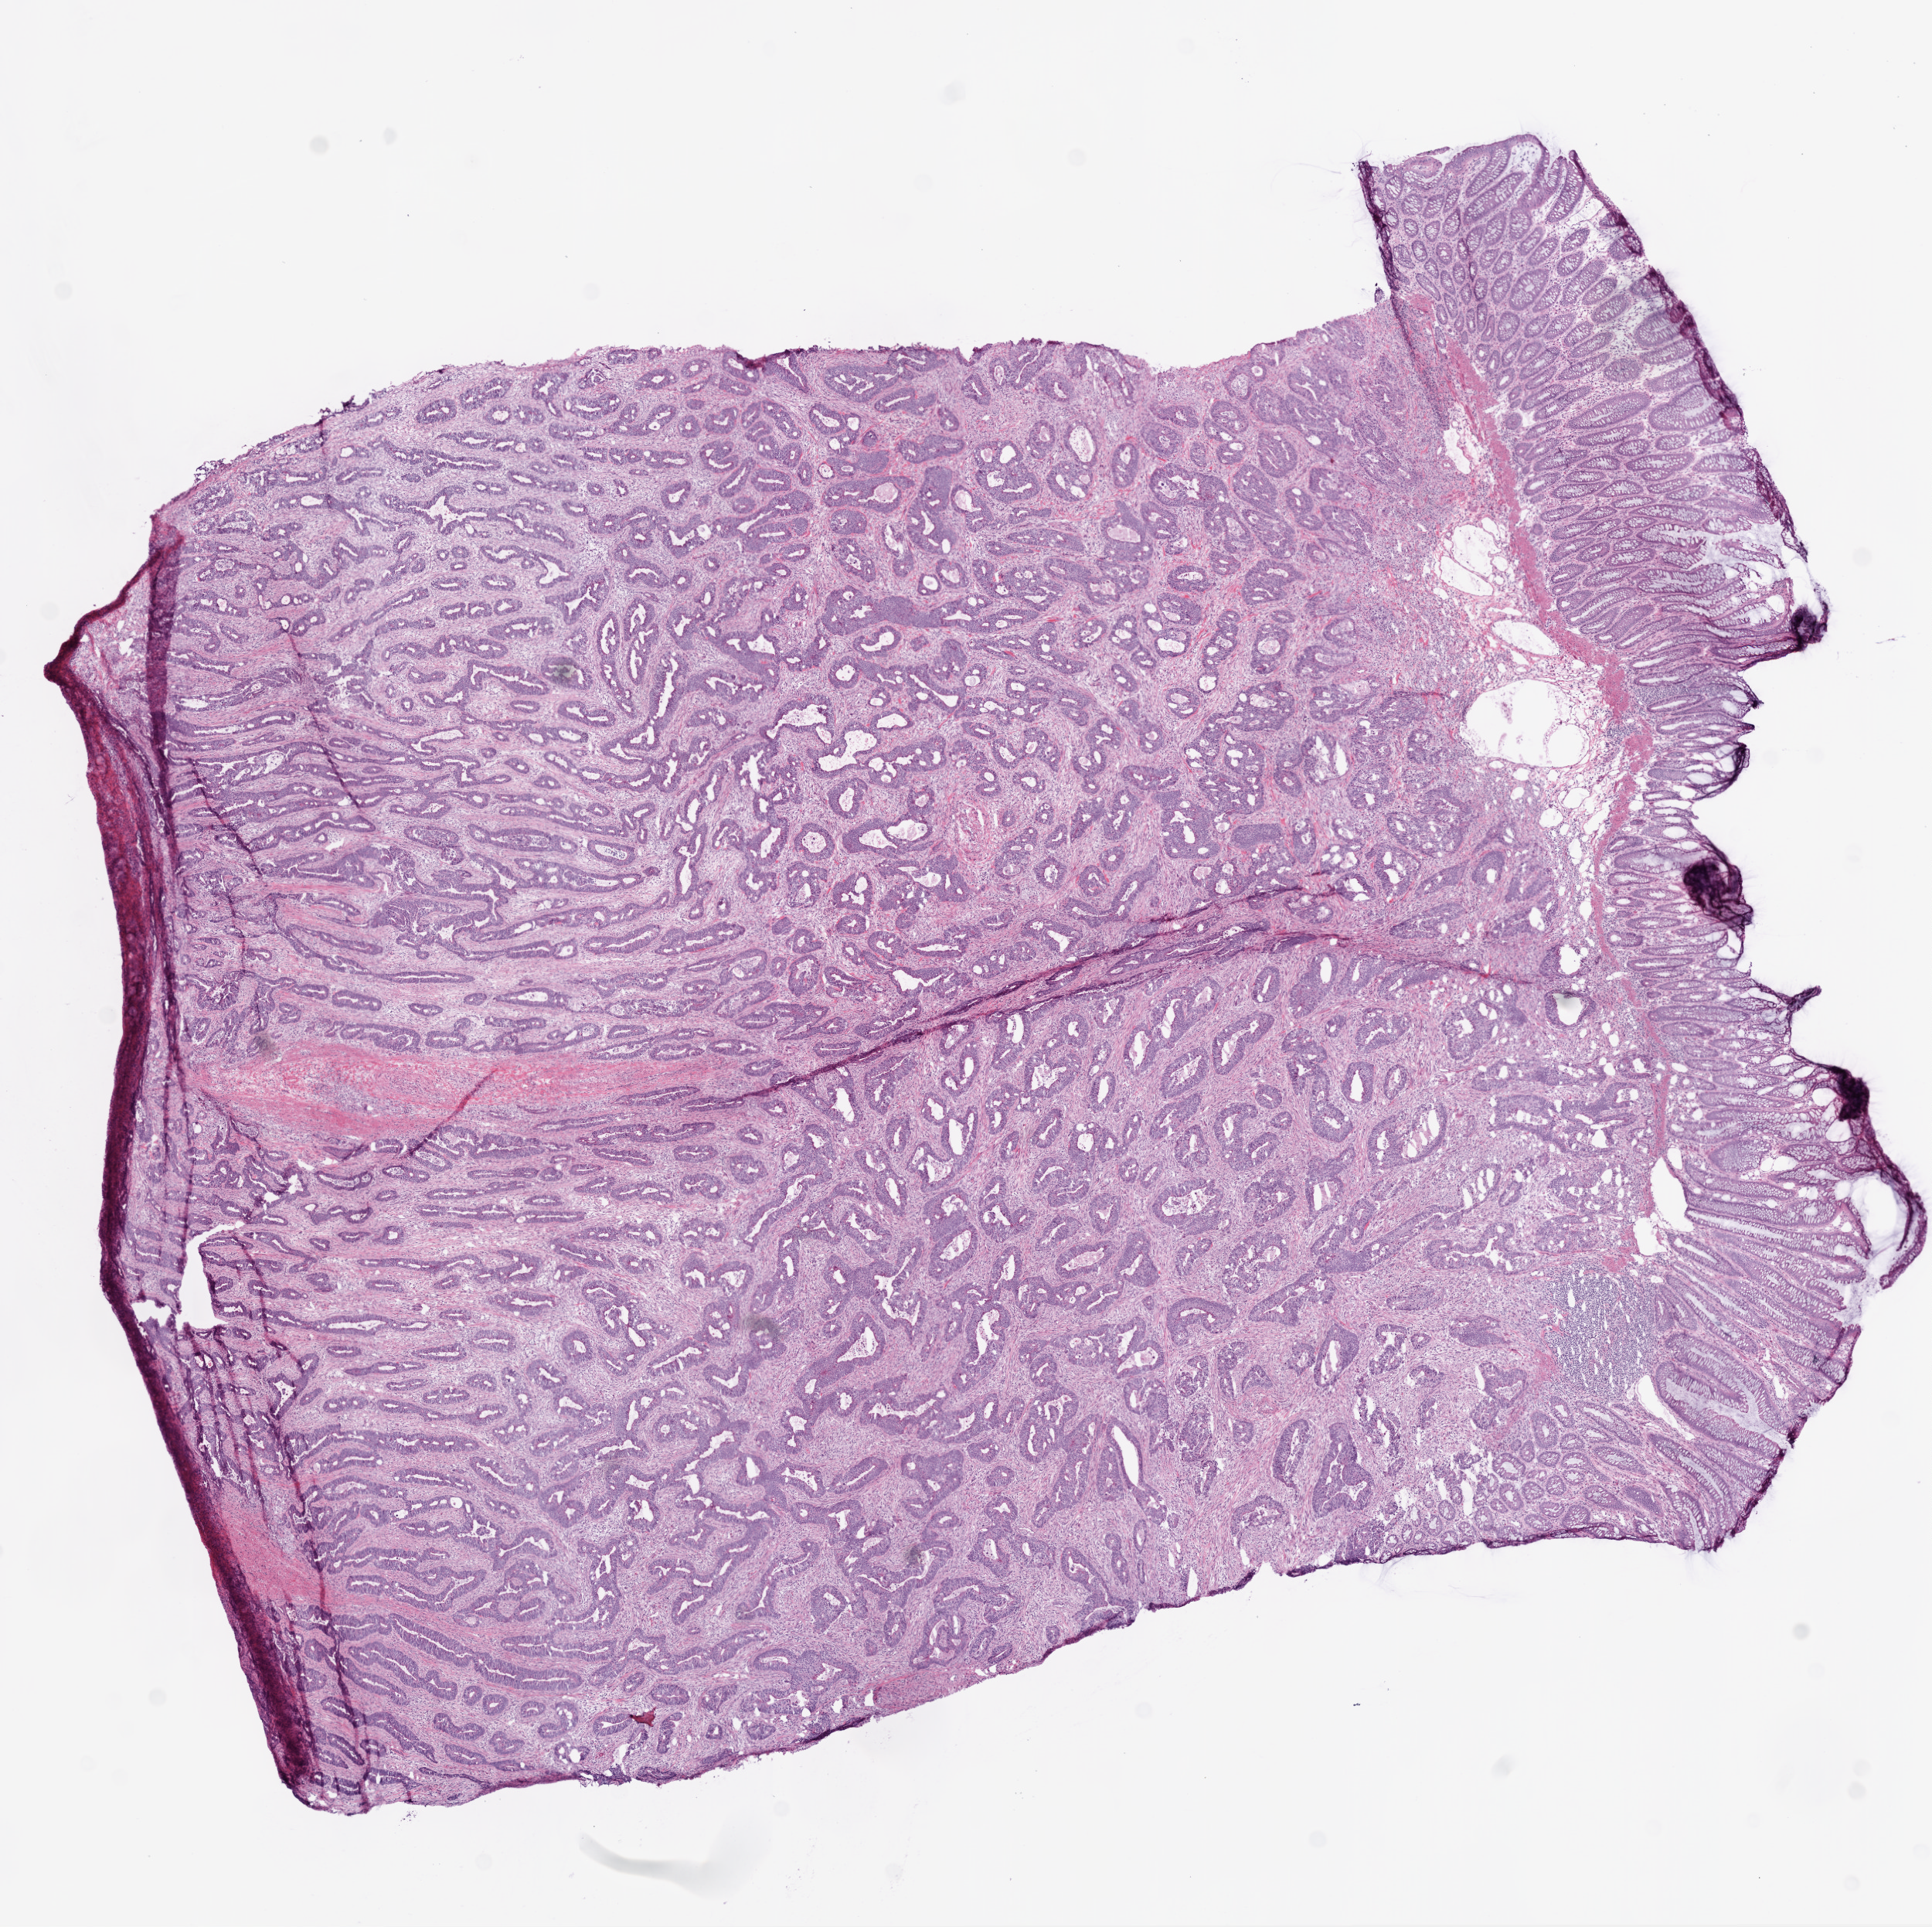
Whole-slide histology image, Hematoxylin and eosin (H&E) stained, whole scanned area (about 10.0 x 10.0 mm) shown as a low-resolution overview, frozen section, primary tumour sample from the colon. Male, age 78 years at initial diagnosis. Pathologist review of this section (percent, as recorded): tumour cells 40%, tumour nuclei 70%, normal cells 50%, stromal cells 10%, necrosis 0%.
AJCC pathologic stage: IIA (6th edition). TNM: T3 N0 MX. Lymph nodes positive (case pathology): 0 of 11 examined. Histologic diagnosis: Adenocarcinoma, NOS (sigmoid colon).